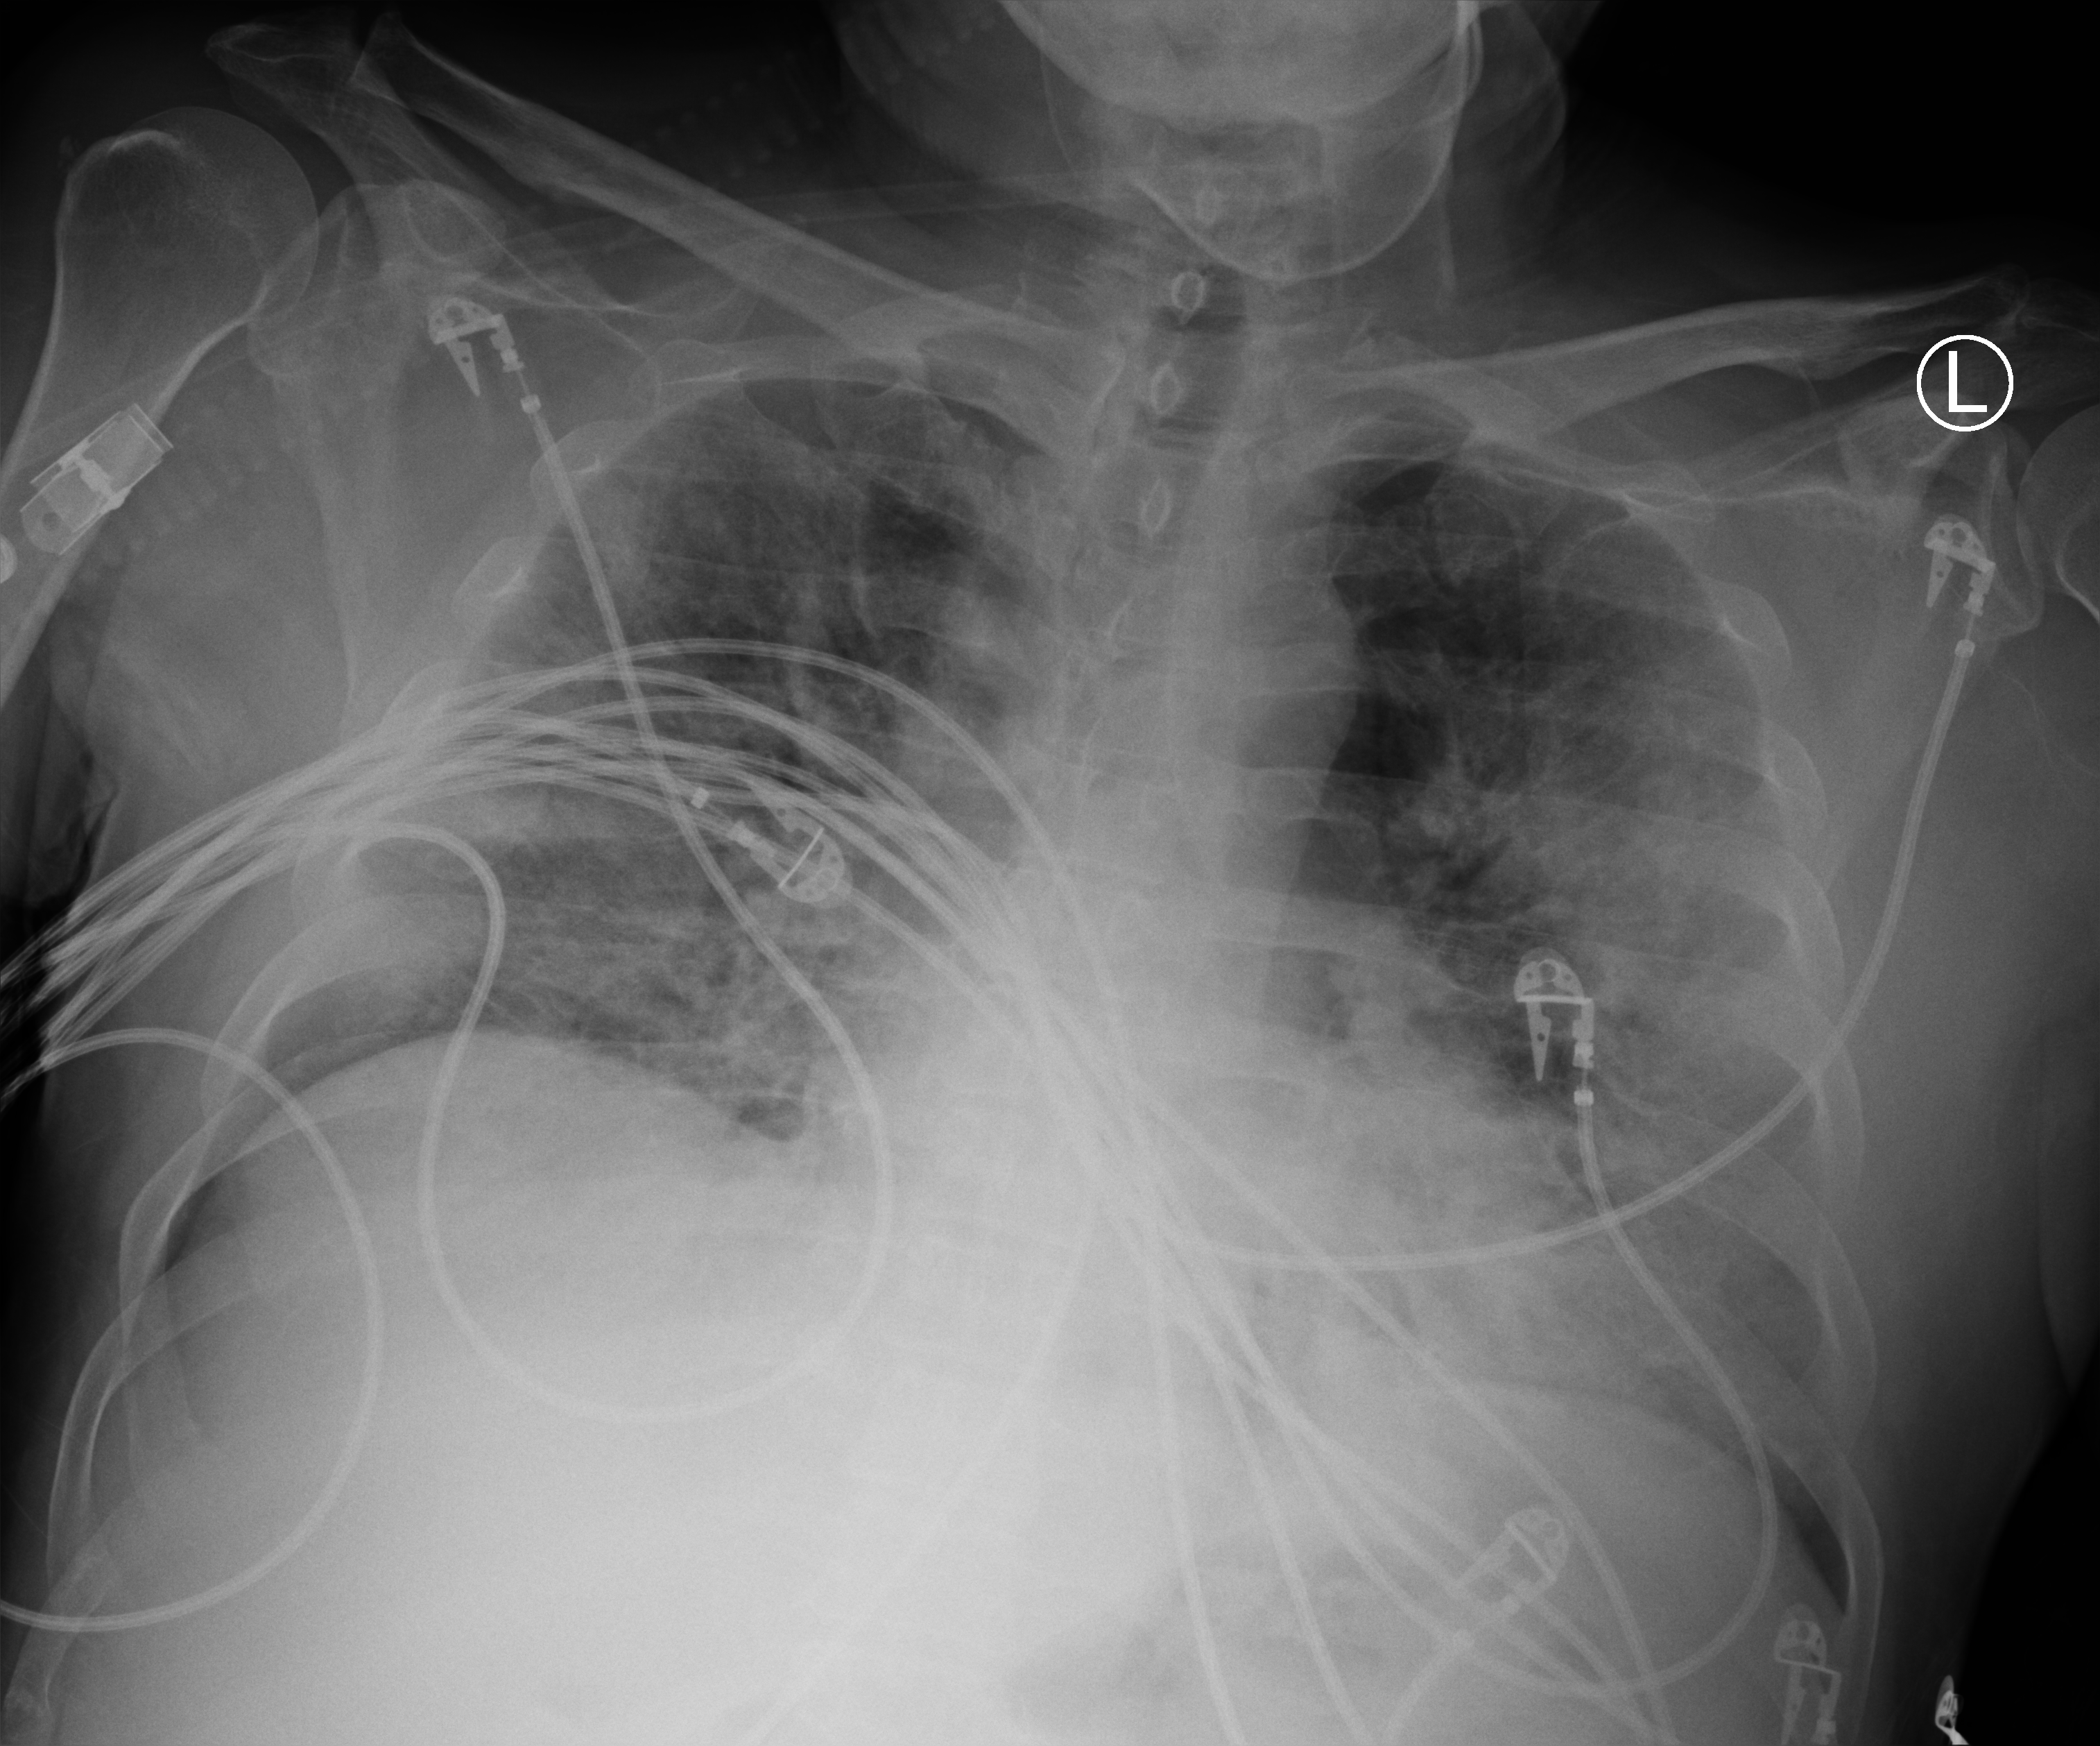
Bedside chest radiograph (computed radiography), anteroposterior (AP) projection. Patient hospitalised with COVID-19; male, aged 18–59 years.
Hospital-stay facts (about this admission, not read from this image; timing relative to this image not recorded): diabetes (admission record): yes; mechanically ventilated during this hospital stay: yes.